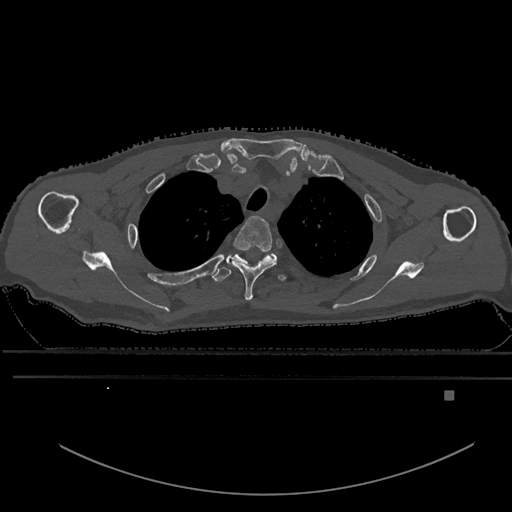
CT including the spine, one axial slice. Position 482 of 969 along the scan axis. Bone window (W 1800 / L 400 HU). 512 × 512 image matrix, field of view 456 × 456 mm. Male patient, age 82 years. From the clinical record (not read from this slice): primary cancer: prostate.
Annotated regions visible in this slice (semi-automatically segmented with operator editing):
- T2 vertebra: bounding box (x1, y1, x2, y2) in pixels: (227, 216, 278, 301)
- T3 vertebra: (212, 254, 287, 282)